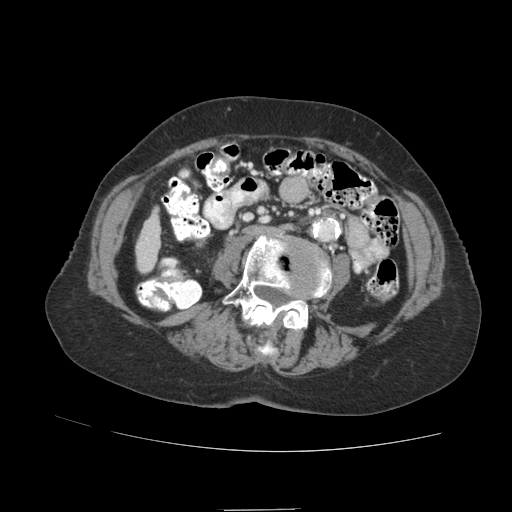
Contrast-enhanced abdominal CT (liver protocol), one axial slice. Position 10 of 89 along the scan axis. Reconstruction kernel STANDARD. Soft-tissue window (W 400 / L 40 HU). 512 × 512 image matrix, field of view 360 × 360 mm. From the clinical record (not read from this slice): diagnosis: hepatocellular carcinoma (patient treated with transarterial chemoembolisation; whether this scan precedes or follows treatment is not stated here); TNM stage (as recorded): Stage-II; Child-Pugh class: A; tumour differentiation: moderately differentiated; tumour nodularity: multinodular.
Outlined on this slice (semi-automatically segmented with operator editing):
- liver parenchyma outside the tumour (the mass and vessels are separate outlines, so this box may not span the whole liver): box from (x=136, y=211) to (x=160, y=272) px